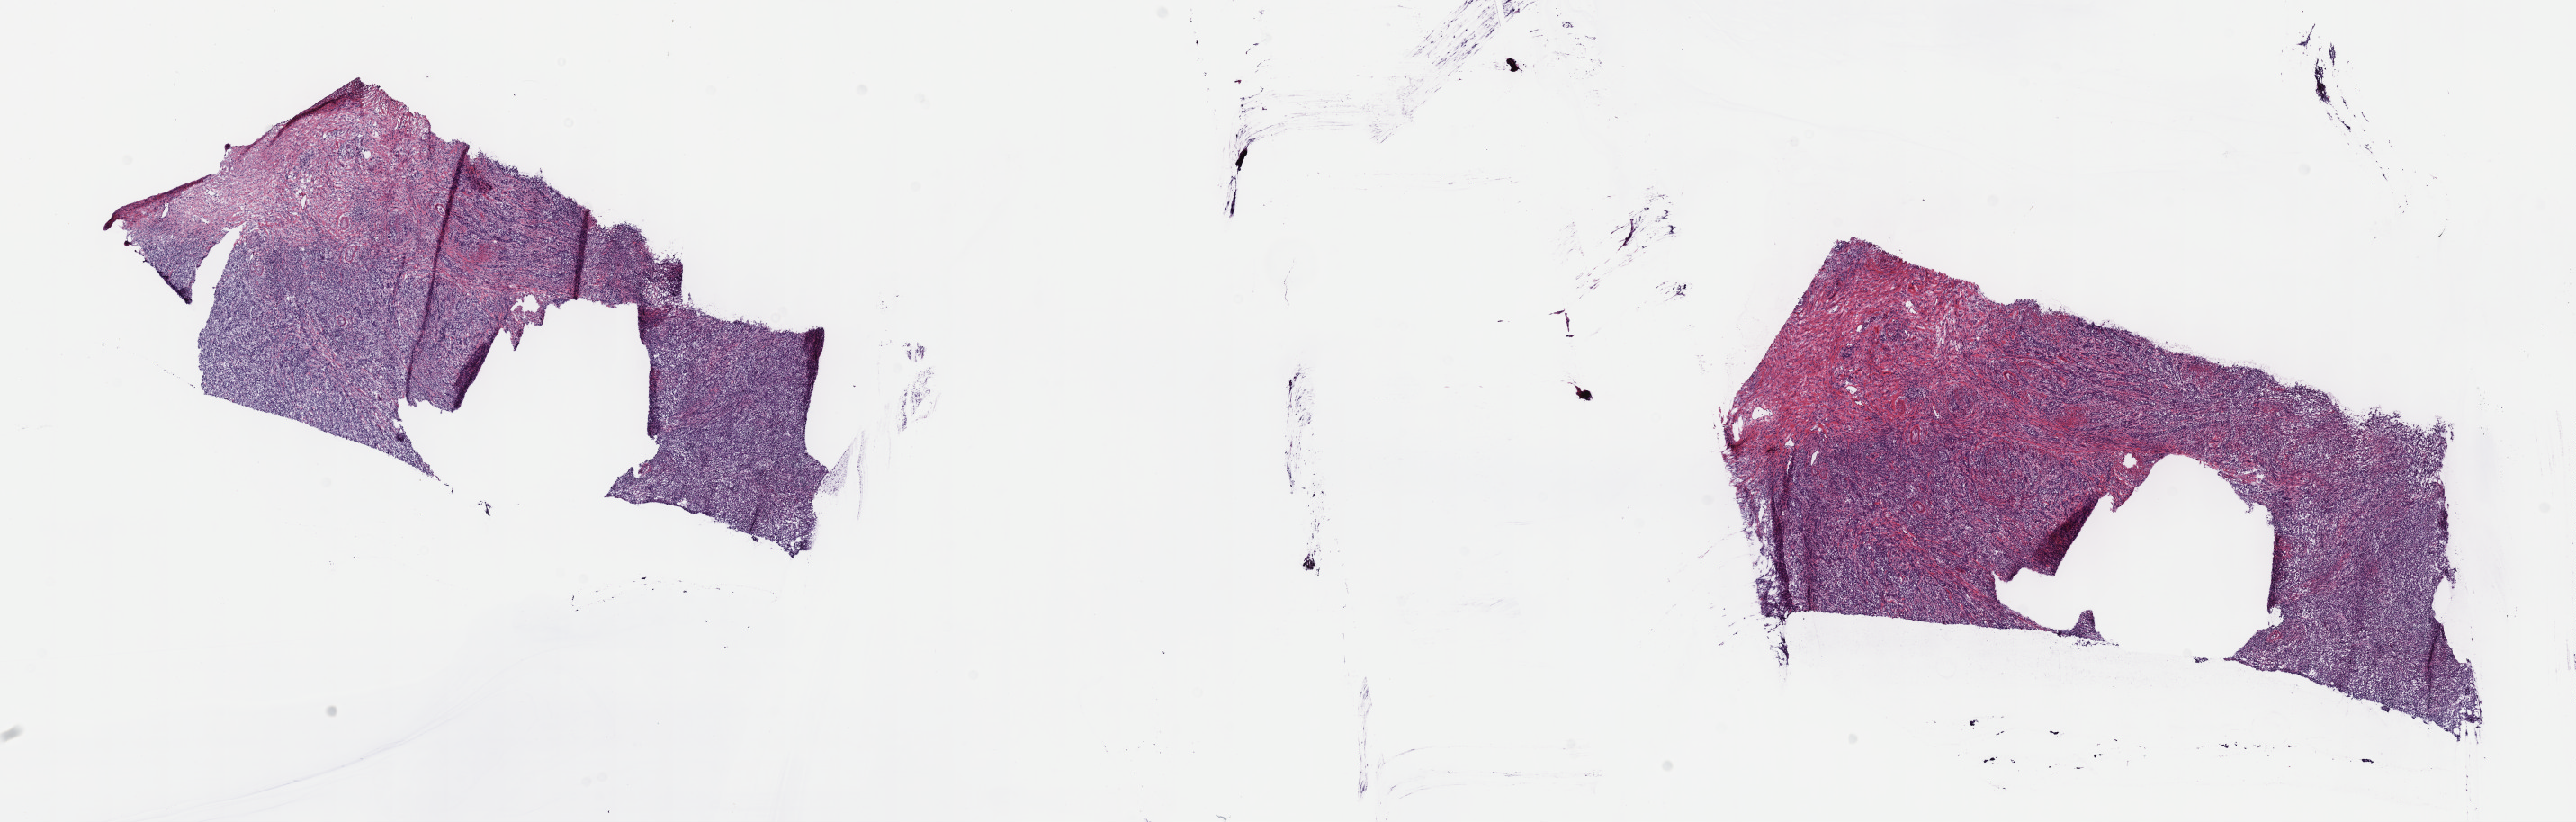
Hematoxylin and eosin (H&E) stained whole-slide image — low-resolution overview of the scanned area, about 23.2 x 7.4 mm (slide scanned at 40x). Frozen section. Sample: primary tumour, bladder. Male patient; age at initial diagnosis 76 years. Histologic grade: high grade. Slide review estimates, as recorded: tumour cells 75%, tumour nuclei 75%, normal cells 0%, stromal cells 25%, necrosis 0%. Inflammatory infiltration, as recorded: lymphocyte infiltration 4%, monocyte infiltration 1%, neutrophil infiltration 4%.
• lymph nodes positive (case pathology): 0 of 104 examined
• pathologic diagnosis: Transitional cell carcinoma
• AJCC pathologic stage: III